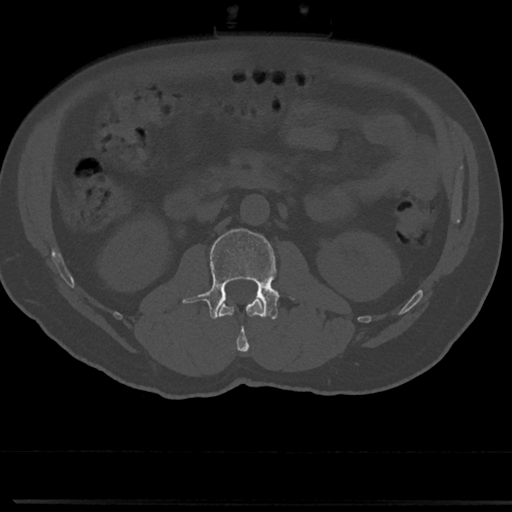
CT including the spine, one axial slice. Position 33 of 817 along the scan axis. Reconstruction kernel Br40s/3. Bone window (W 1800 / L 400 HU). 0.5 mm slice thickness. 512 × 512 image matrix, field of view 355 × 355 mm. Male patient, age 61 years. From the clinical record (not read from this slice): primary cancer: prostate.
Annotated regions visible in this slice (semi-automatically segmented with operator editing):
- L1 vertebra: bounding box <219,298,263,354> (left, top, right, bottom; pixels)
- L2 vertebra: <191,228,278,319>